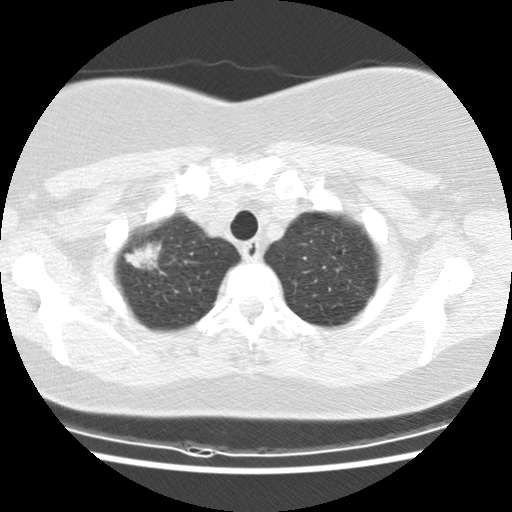
Low-dose screening chest CT, axial slice. Baseline annual screen. Lung window (W 1500 / L -600 HU). Standard (soft-tissue) reconstruction kernel (STANDARD). 120 kVp. Female participant, aged 61 years at enrolment.
Expert-annotated lung lesion, box from (x=114, y=230) to (x=174, y=285) px. The exam's reader record, not a measurement of the box and not confirmed to be the same lesion: non-calcified nodule or mass ≥4 mm, right upper lobe, 26 × 16 mm, spiculated (stellate) margins, mixed attenuation. Official screen result: positive, change unspecified: nodule(s) >= 4 mm or enlarging nodule(s), mass(es), or other non-specific abnormalities suspicious for lung cancer.